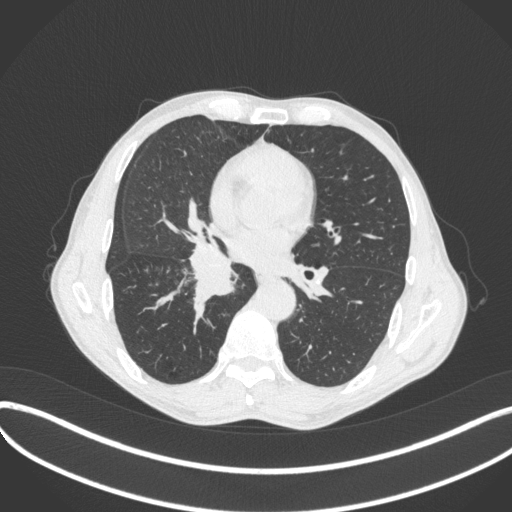
Chest CT, one axial slice; 120 kVp; lung window (W 1500 / L -600 HU); 1 mm slice thickness; 512 × 512 image matrix, field of view 400 × 400 mm. Patient: male, 65 years. From the clinical record (not read from this slice): clinical TNM (as recorded): T2a N0 M0; histopathological grade: G2.
Annotated regions visible in this slice (rectangle marked by the reading radiologist):
- lung tumour (recorded histology: squamous cell carcinoma): bounding box (x1, y1, x2, y2) in pixels: (185, 237, 240, 301)